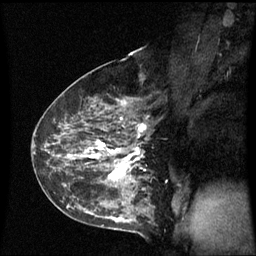
Breast MRI (dynamic contrast-enhanced), one sagittal slice. Position 36 of 60 along the scan axis. Dynamic contrast-enhanced series, image 2 of 3 at this slice position (ordered by acquisition). 1.5 T. TE 4.2 ms, TR 8.9 ms. 256 × 256 image matrix, field of view 210 × 210 mm. Patient: female, 43 years. Case-level facts recorded for this patient, not image findings: setting: breast cancer imaged before/during neoadjuvant chemotherapy; receptor status: HER2-positive.
Structures marked on this image (semi-automatically segmented with operator editing):
- analysis volume of interest (the breast-tissue region the enhancement analysis was run in; not a lesion): bounding box (x1, y1, x2, y2) in pixels: (56, 80, 148, 195)
- tumour enhancement mask (voxels above the 70 % enhancement threshold inside the analysis volume of interest): (68, 100, 145, 181)